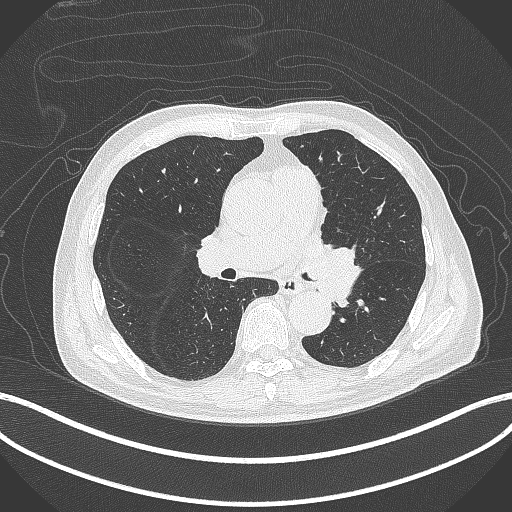
Chest CT, one axial slice. Position 238 of 417 along the scan axis. 120 kVp. Lung window (W 1500 / L -600 HU). 1 mm slice thickness. 512 × 512 image matrix. Male patient, age 77 years. From the clinical record (not read from this slice): clinical TNM (as recorded): T3 N1 M0.
Annotated regions visible in this slice (bounding box drawn by a radiologist):
- lung tumour (recorded histology: adenocarcinoma): bounding box <307,243,361,308> (left, top, right, bottom; pixels)